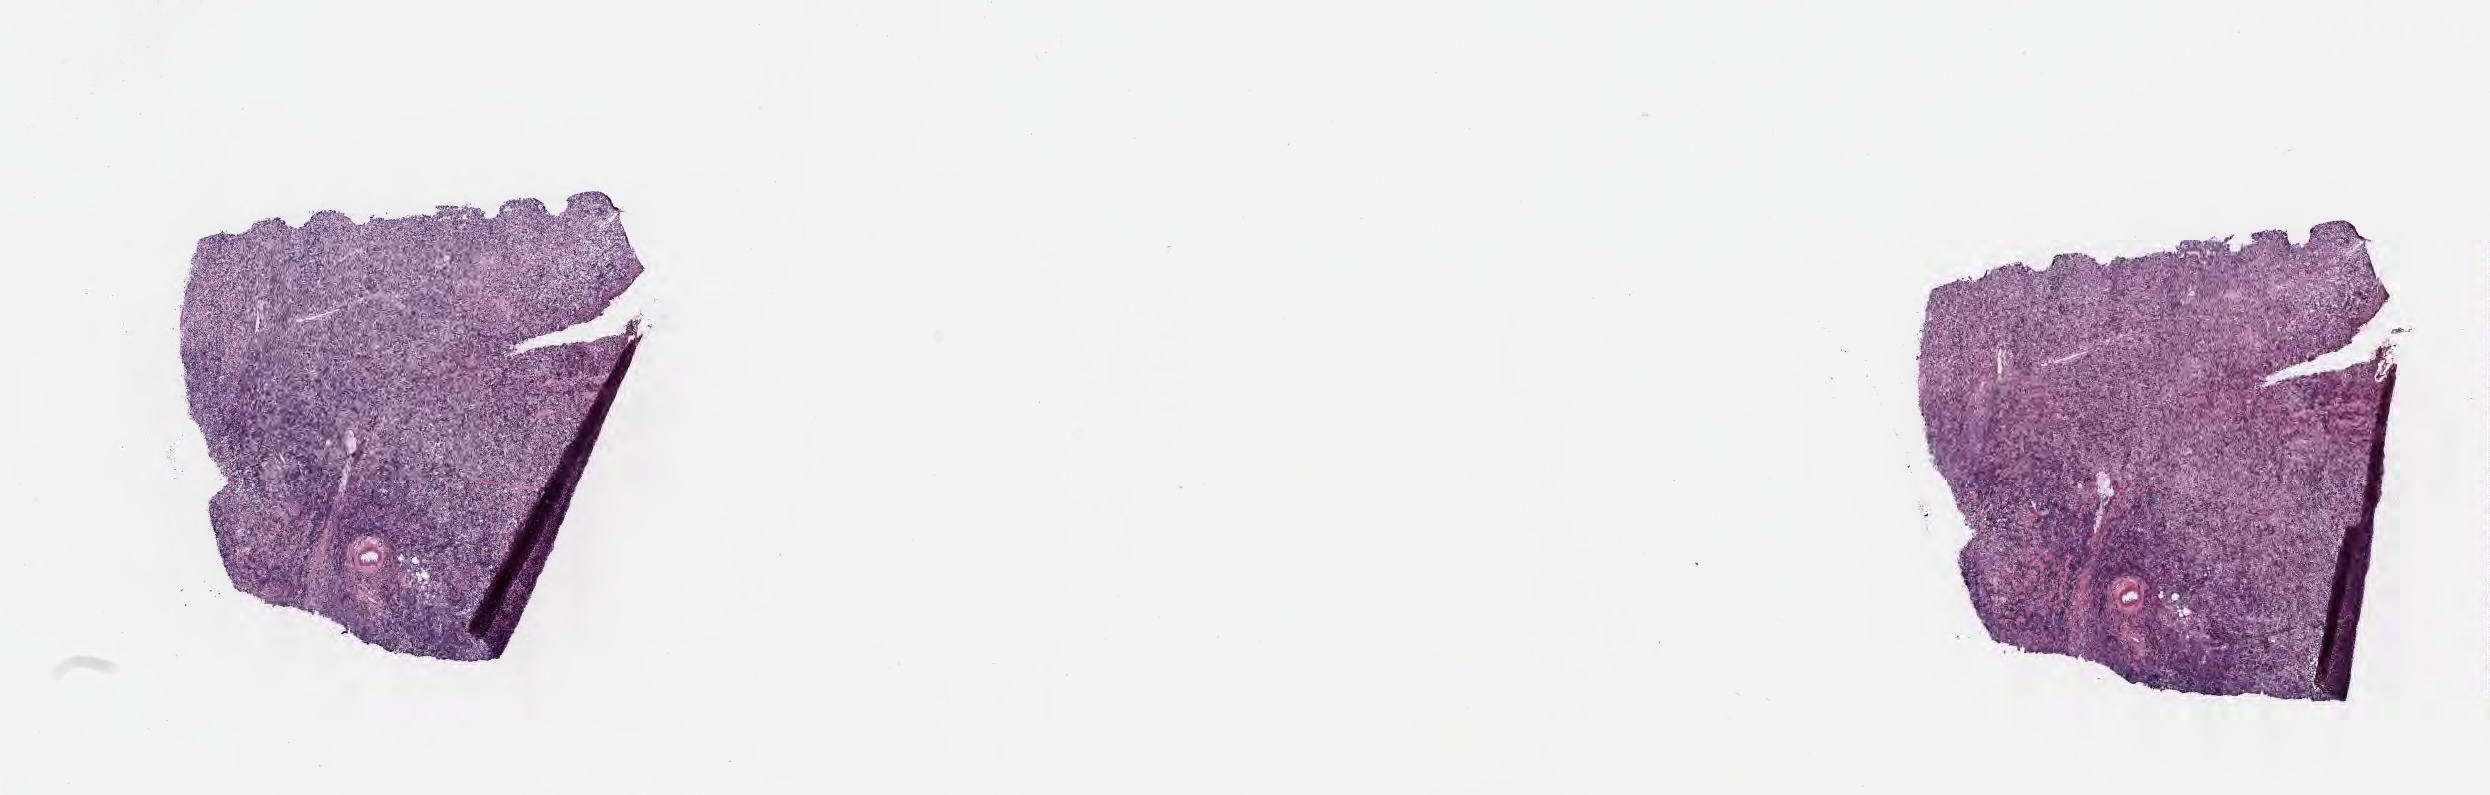
Hematoxylin and eosin (H&E) whole-slide image — low-resolution overview of the scanned area, about 20.1 x 6.4 mm, frozen section (tissue freezing medium), primary tumor, anatomic site: colon. Patient female; aged 12. Slide review estimates, as recorded: tumor cells 90%, tumor nuclei 95%, stromal cells 5%, necrosis 5%, normal cells 0%. Inflammatory infiltration, as recorded: lymphocyte infiltration 40%, monocyte infiltration 25%, neutrophil infiltration 10%.
* histologic diagnosis: Burkitt lymphoma, NOS
* Ann Arbor stage (patient): Stage III